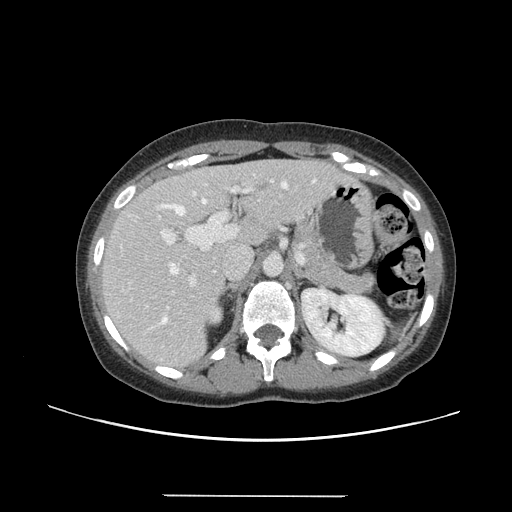
Contrast-enhanced abdominal CT, one axial slice; position 89 of 144 along the scan axis; 120 kVp; soft-tissue window (W 400 / L 40 HU); 512 × 512 image matrix, field of view 380 × 380 mm. Female patient, age 53 years. Case-level facts recorded for this patient, not image findings: diagnosis: colorectal cancer liver metastases, imaged before liver resection; multiple liver metastases: yes; largest metastasis: 1.1 cm.
Outlined on this slice (expert manual segmentation):
- hepatic veins: box from (x=161, y=180) to (x=315, y=323) px
- liver: (x=102, y=160)–(x=345, y=368)
- planned liver remnant (the part of the liver to remain after resection): (x=102, y=160)–(x=313, y=297)
- portal vein (with intrahepatic branches): (x=130, y=179)–(x=274, y=287)